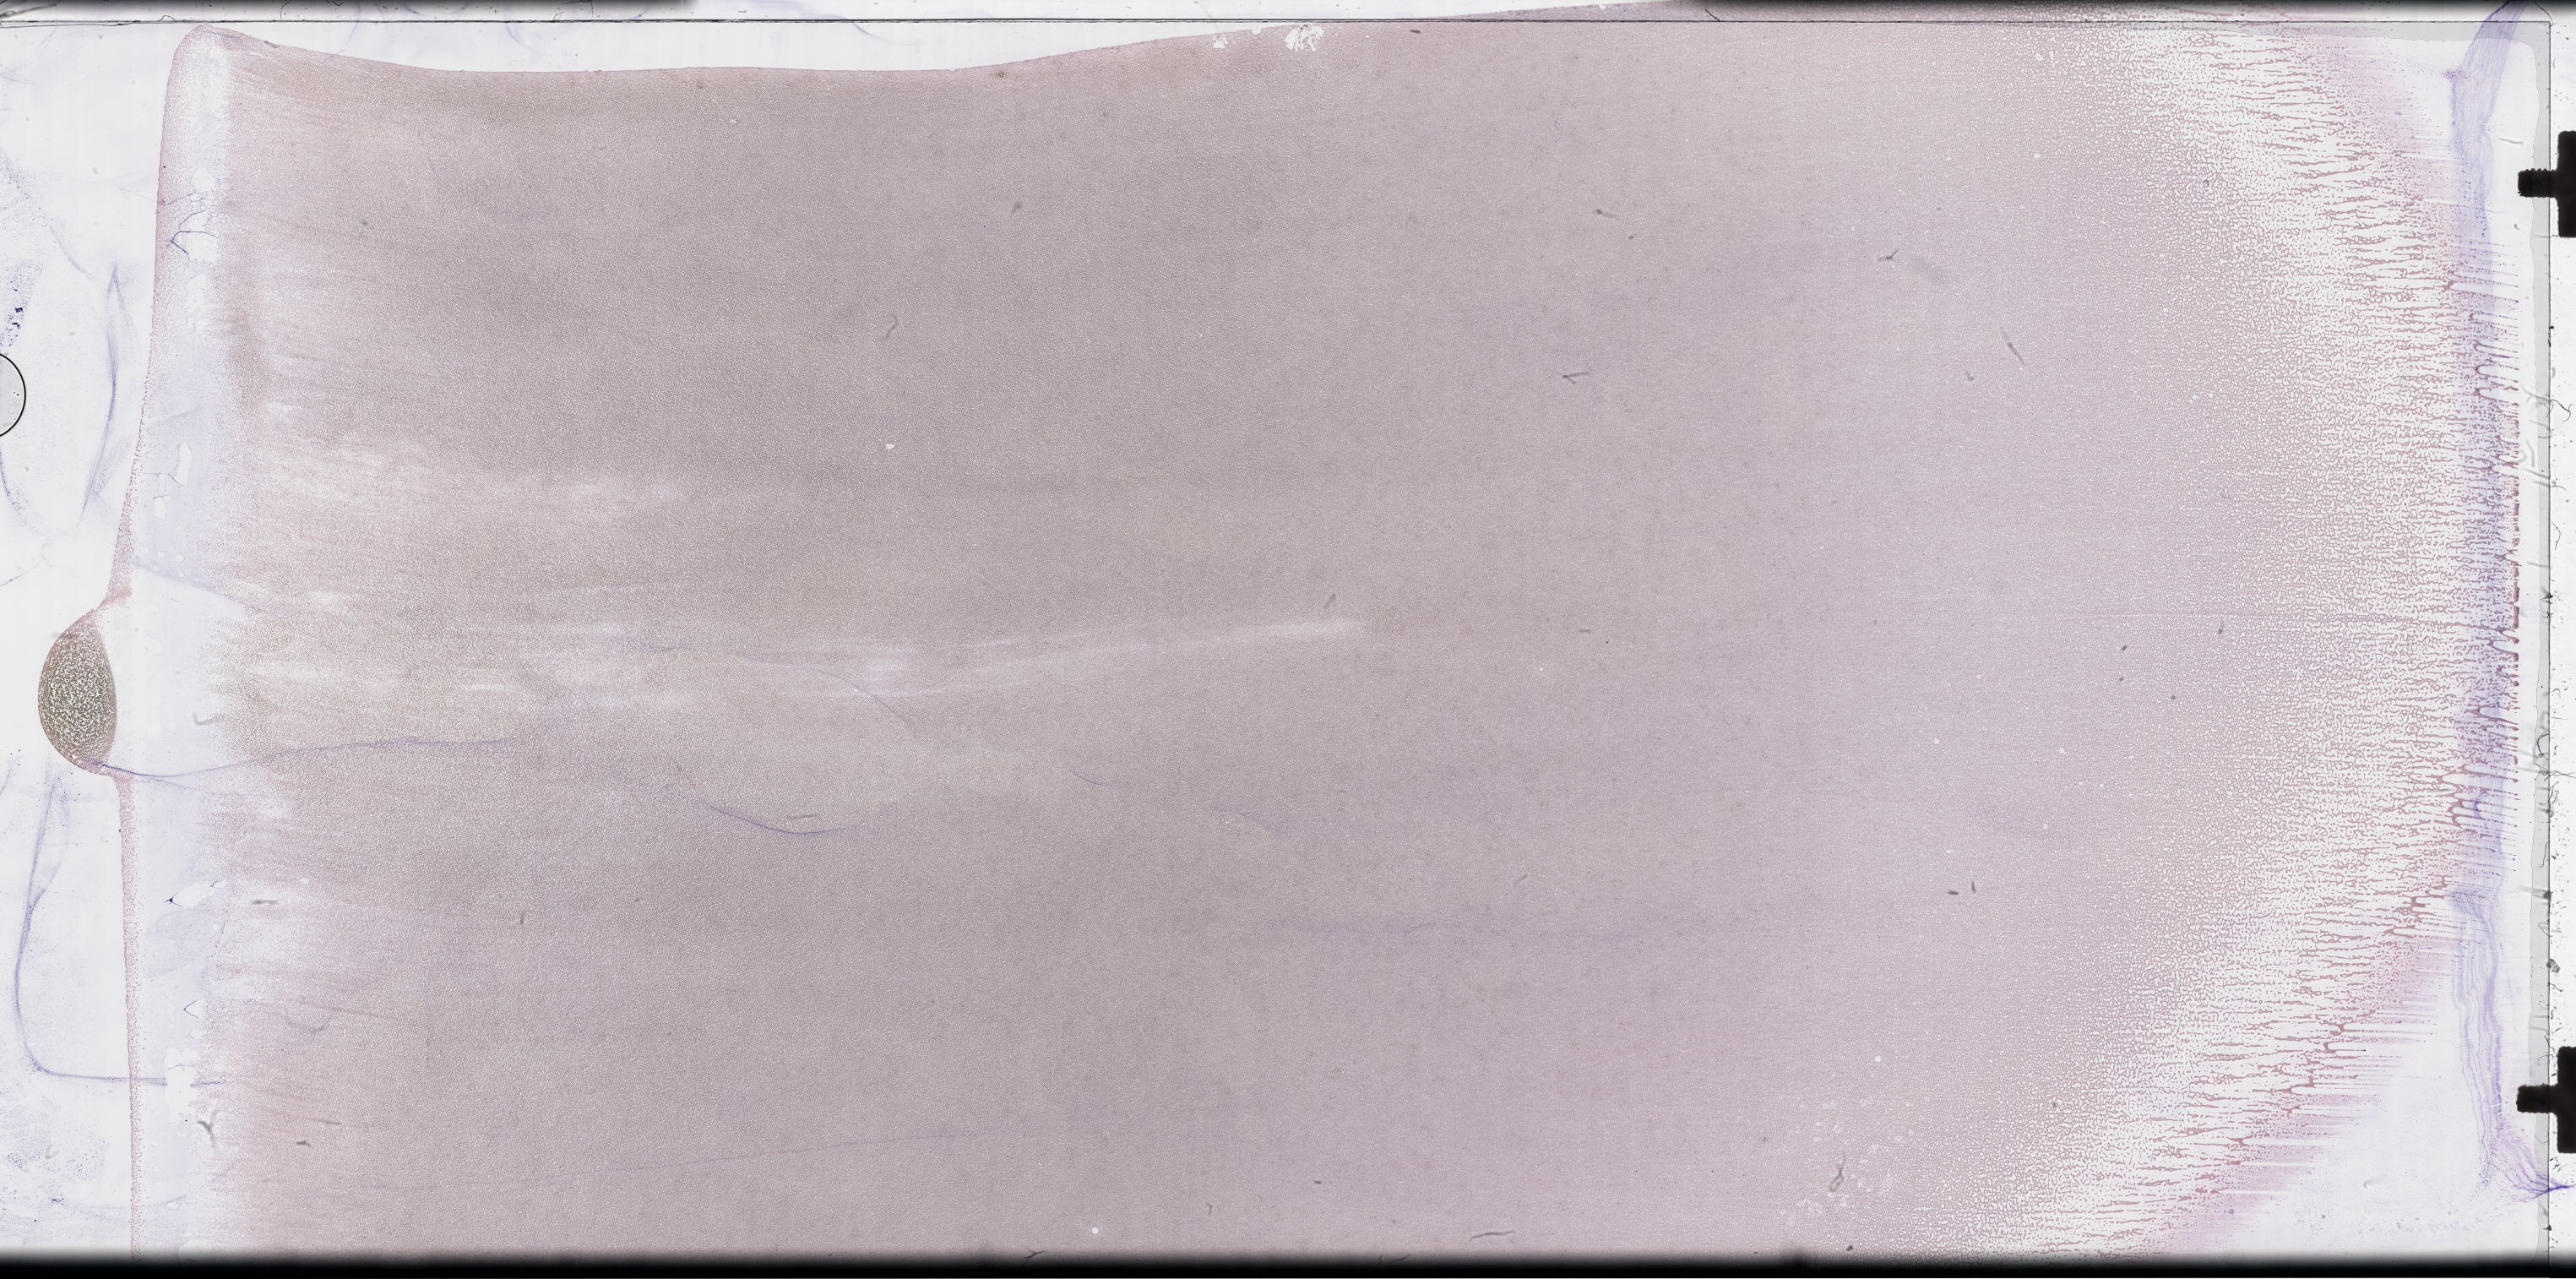
Wright–Giemsa-stained whole blood smear, whole-slide image — low-resolution overview of the scanned area, about 49.3 x 24.4 mm. Smear from an EDTA sample. Collected on treatment. Patient sex: male.
- from a patient with: Plasma Cell Myeloma